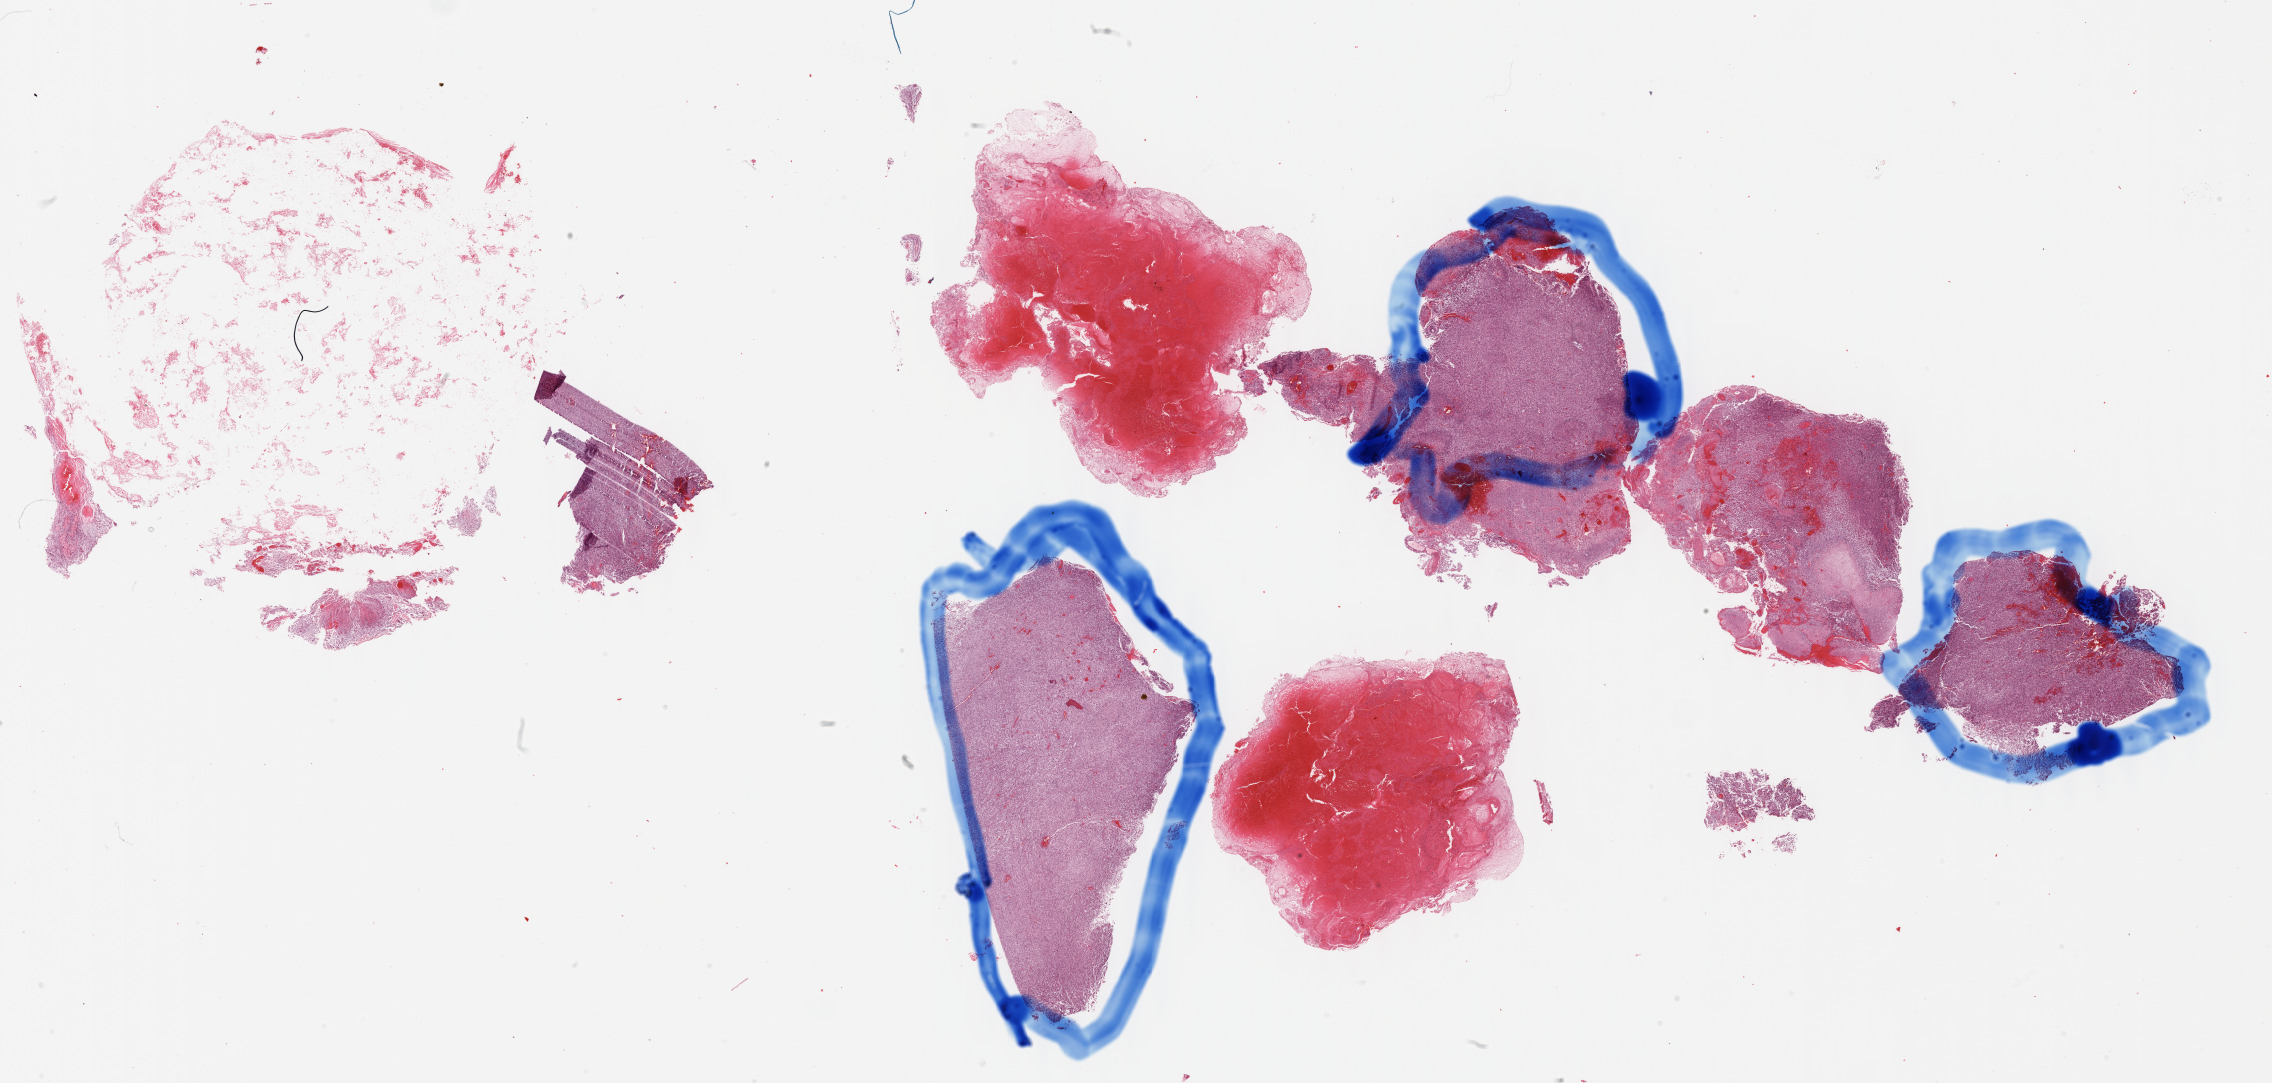
Whole-slide histology image, H&E-stained, whole scanned area (about 36.7 x 17.5 mm) shown as a low-resolution overview, FFPE section, primary tumour sample from the brain. Male patient; age at initial diagnosis 69 years.
Diagnosis: Glioblastoma.